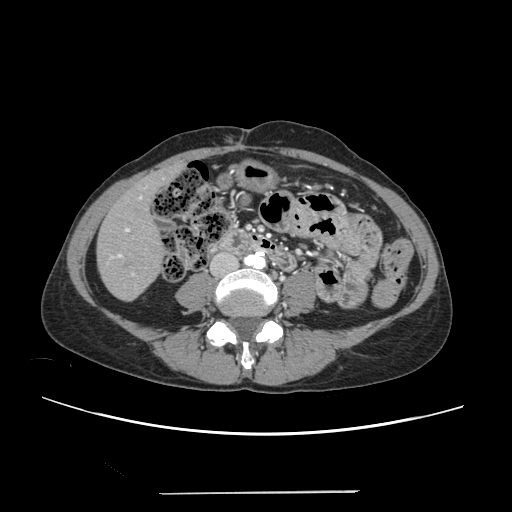
Contrast-enhanced abdominal CT, one axial slice. Slice 53 of 240 in the series (ordered by position). Intravenous contrast given. Soft-tissue window (W 400 / L 40 HU). 512 × 512 image matrix. Female patient, age 60 years. From the clinical record (not read from this slice): diagnosis: colorectal cancer liver metastases, imaged before liver resection; multiple liver metastases: no; largest metastasis: 1.5 cm.
Outlined on this slice (expert manual segmentation):
- liver: bounding box [x1, y1, x2, y2] px = [97, 168, 178, 300]
- planned liver remnant (the part of the liver to remain after resection): [97, 171, 170, 300]
- portal vein (with intrahepatic branches): [110, 186, 146, 275]